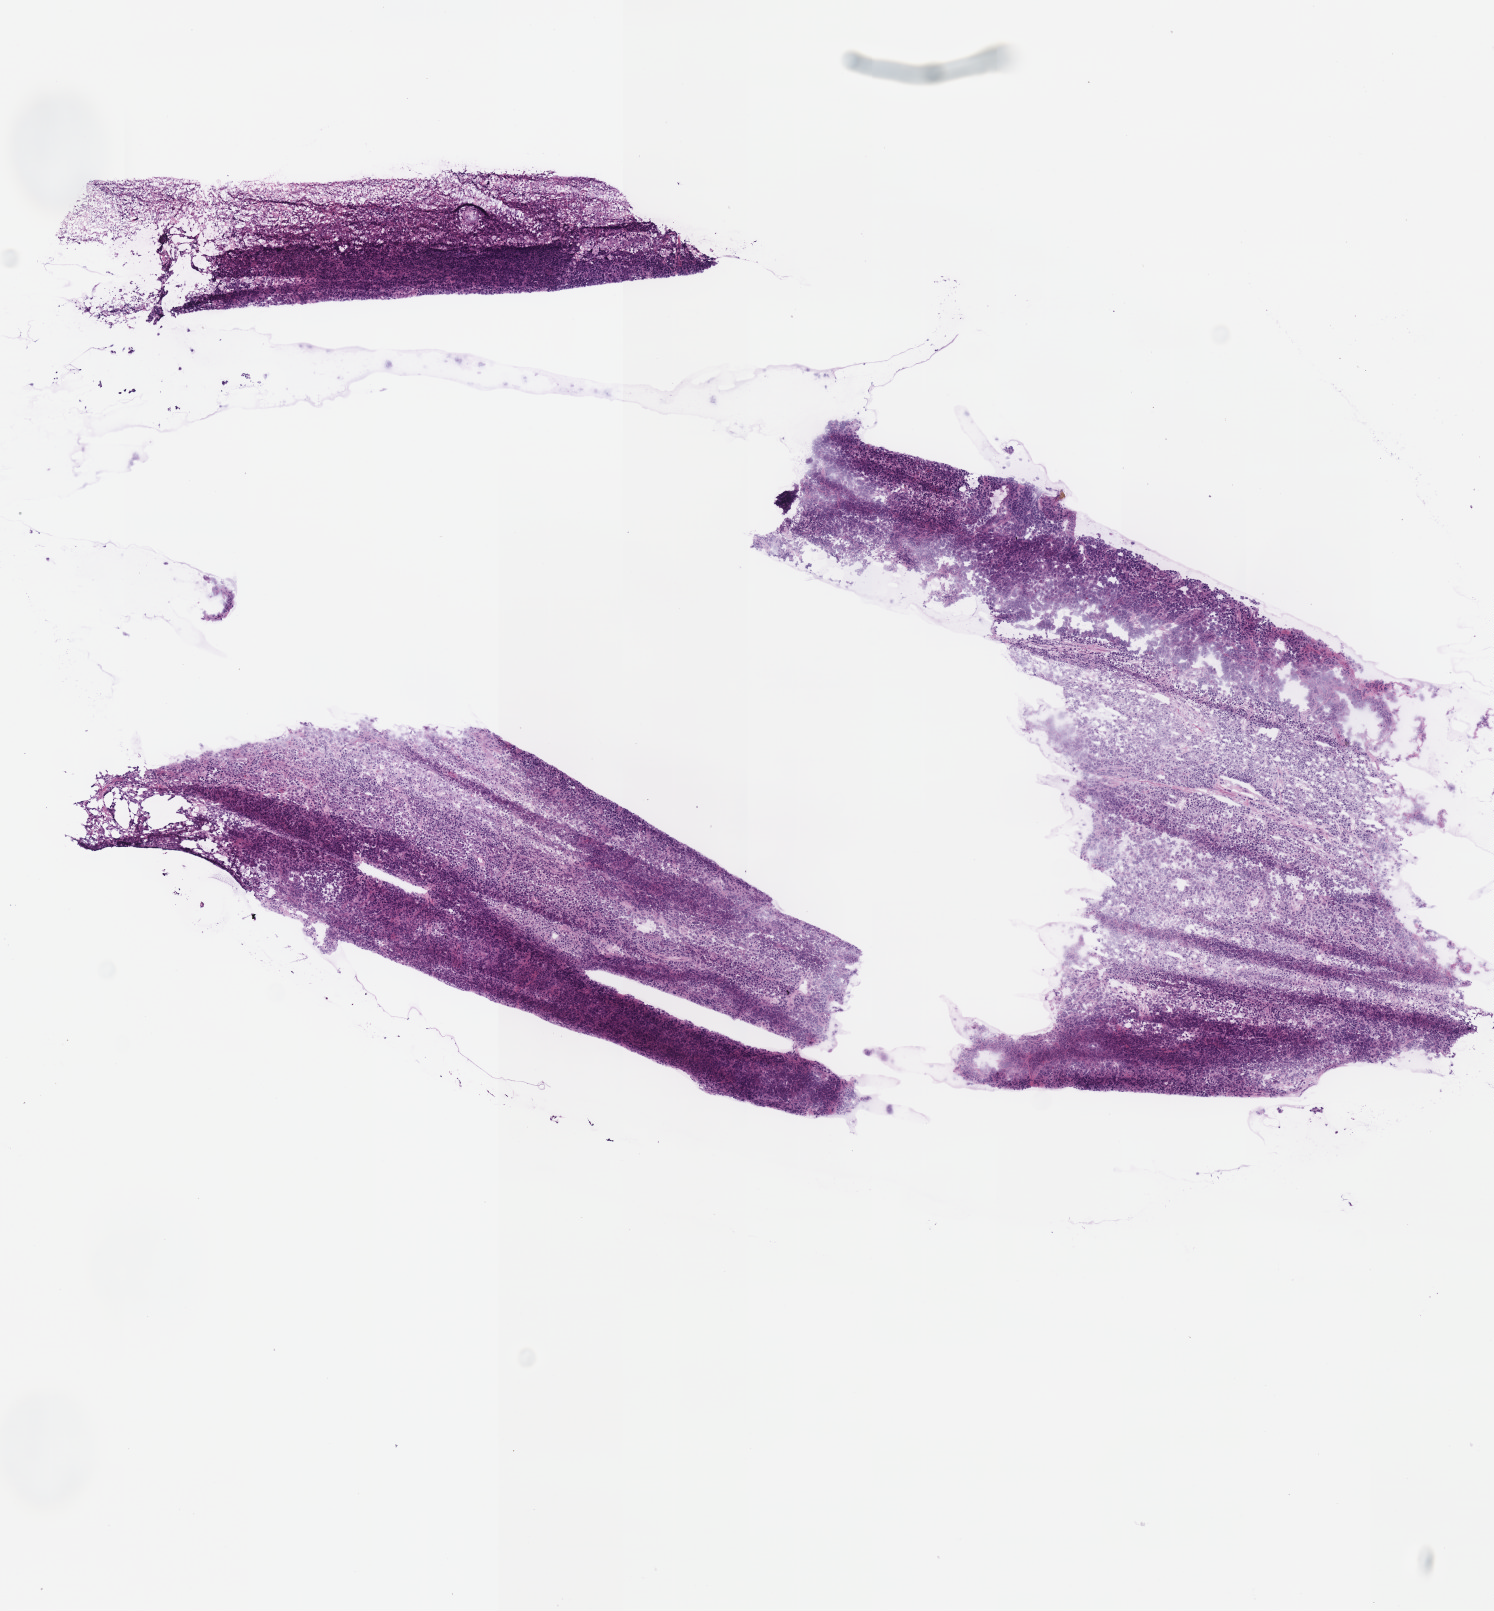
Digitized Hematoxylin and eosin (H&E) stained tissue section (whole slide), low-resolution overview of the scanned area, about 5.9 x 6.3 mm; frozen section; stomach, primary tumour sample. Patient: male, age at initial diagnosis 70 years. Slide review estimates, as recorded: tumour cells 95%, tumour nuclei 60%.
Histologic diagnosis: Carcinoma, diffuse type (body of stomach).